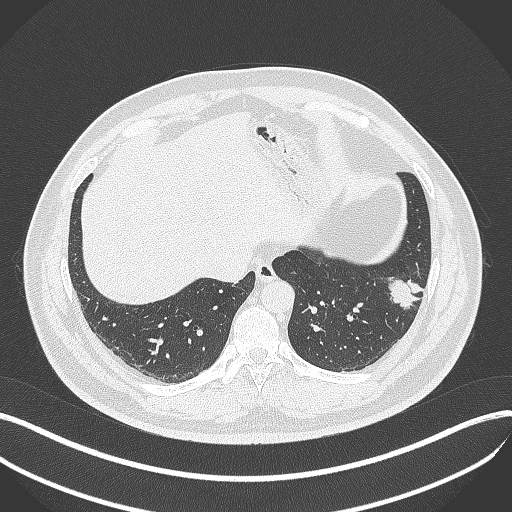
Chest CT, one axial slice; position 115 of 429 along the scan axis; 120 kVp; lung window (W 1500 / L -600 HU); 1 mm slice thickness; 512 × 512 image matrix. Male patient, age 39 years. From the clinical record (not read from this slice): clinical TNM (as recorded): T2a N0 M0.
Annotated regions visible in this slice (bounding box drawn by a radiologist):
- lung tumour (recorded histology: adenocarcinoma): bounding box (x1, y1, x2, y2) in pixels: (384, 271, 426, 312)